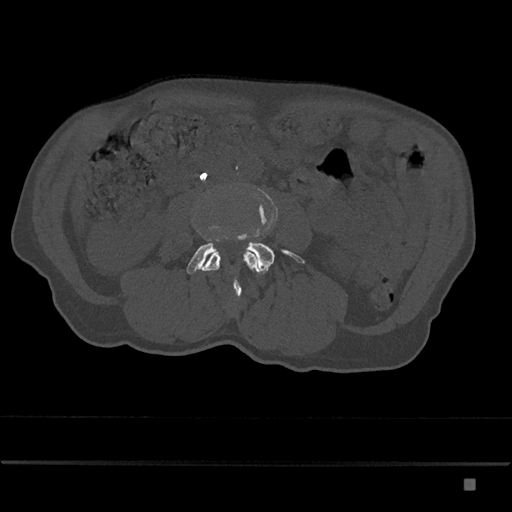
CT including the spine, one axial slice. Reconstruction kernel Br40s/3. 120 kVp. Bone window (W 1800 / L 400 HU). 0.5 mm slice thickness. 512 × 512 image matrix, field of view 390 × 390 mm. Patient: male, 72 years. From the clinical record (not read from this slice): primary cancer: prostate.
Annotated regions visible in this slice (semi-automatically segmented with operator editing):
- L3 vertebra: box from (x=202, y=251) to (x=259, y=299) px
- L4 vertebra: (x=186, y=232)–(x=304, y=275)